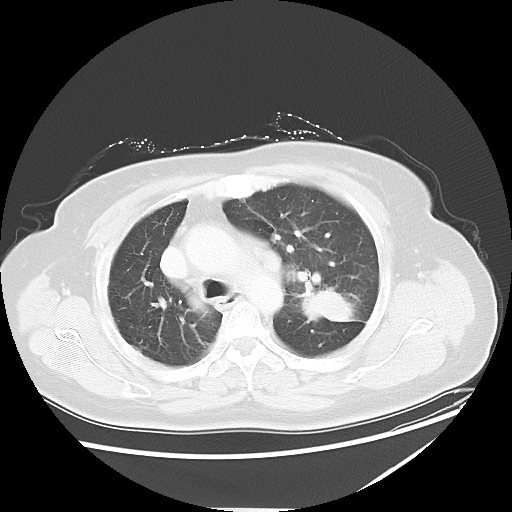
Chest CT, one axial slice. Reconstruction kernel LUNG. 120 kVp. Lung window (W 1500 / L -600 HU). 5 mm slice thickness. 512 × 512 image matrix. Patient: female, 61 years. Case-level facts recorded for this patient, not image findings: clinical TNM (as recorded): T1c N3 M1.
Structures marked on this image (bounding box drawn by a radiologist):
- lung tumour (recorded histology: adenocarcinoma): bounding box <296,283,367,324> (left, top, right, bottom; pixels)